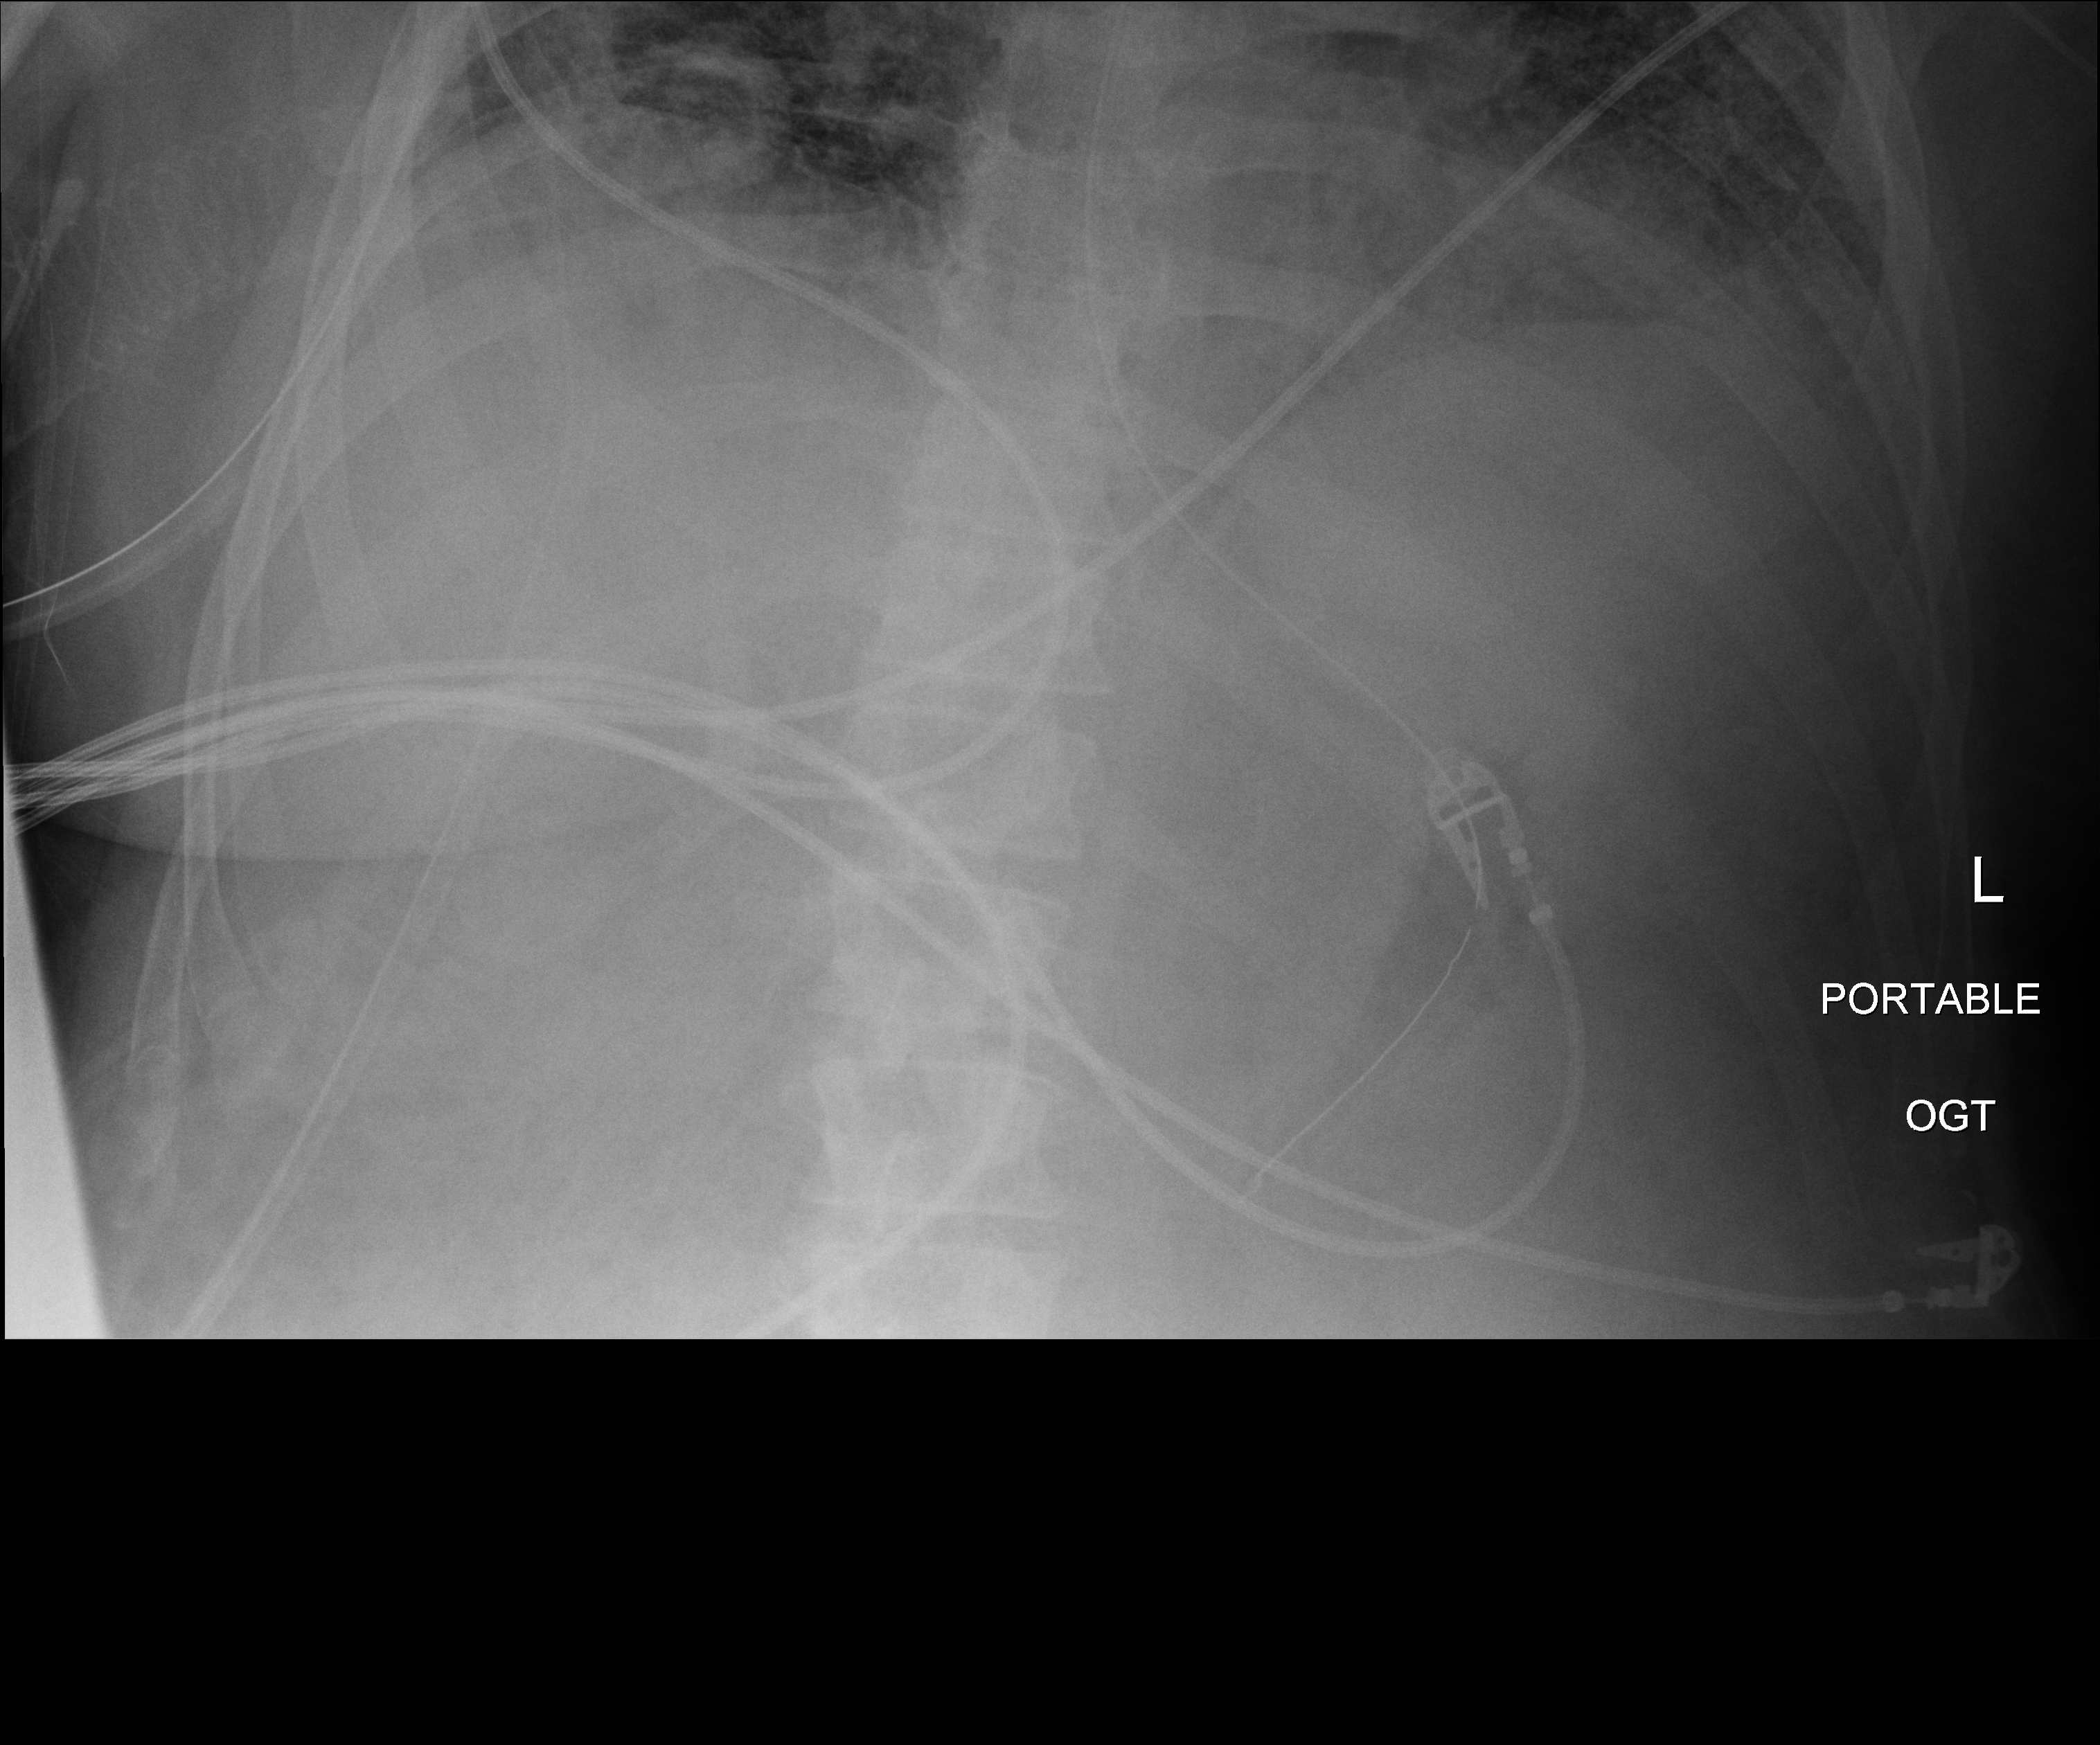
Chest radiograph, anteroposterior (AP) projection. Patient hospitalised with COVID-19; male, aged 18–59 years.
Admission-level facts for this patient (not findings on this image; timing relative to this image not recorded): other chronic lung disease (admission record): no.